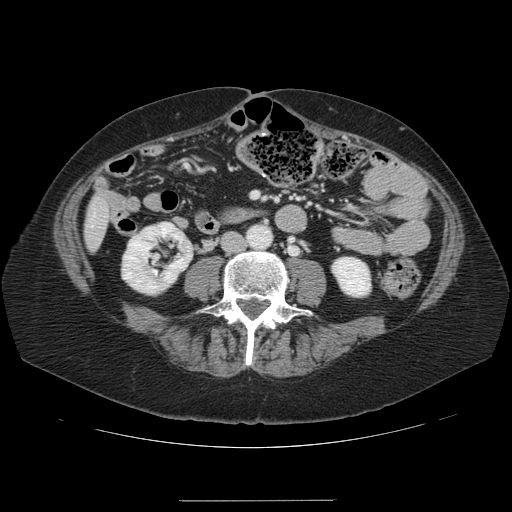
Contrast-enhanced abdominal CT, one axial slice; slice 14 of 141 in the series (ordered by position); 120 kVp; intravenous contrast given; soft-tissue window (W 400 / L 40 HU); 2.5 mm slice thickness; 512 × 512 image matrix. Female patient, age 74 years. From the clinical record (not read from this slice): diagnosis: colorectal cancer liver metastases, imaged before liver resection; multiple liver metastases: yes; largest metastasis: 7 cm; disease in both lobes: yes.
Outlined on this slice (manually delineated by an expert):
- liver: bounding box [x1, y1, x2, y2] px = [86, 198, 110, 249]
- planned liver remnant (the part of the liver to remain after resection): [88, 204, 110, 249]